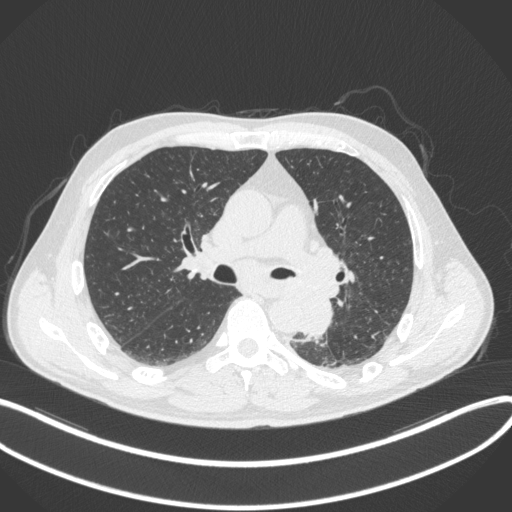
Chest CT, one axial slice. Slice 205 of 328 in the series (ordered by position). Reconstruction kernel B31f. 120 kVp. Lung window (W 1500 / L -600 HU). 1 mm slice thickness. 512 × 512 image matrix. Male patient, age 59 years. Case-level facts recorded for this patient, not image findings: clinical TNM (as recorded): T2a N2 M0.
Structures marked on this image (bounding box drawn by a radiologist):
- lung tumour (recorded histology: squamous cell carcinoma): box from (x=298, y=286) to (x=337, y=340) px